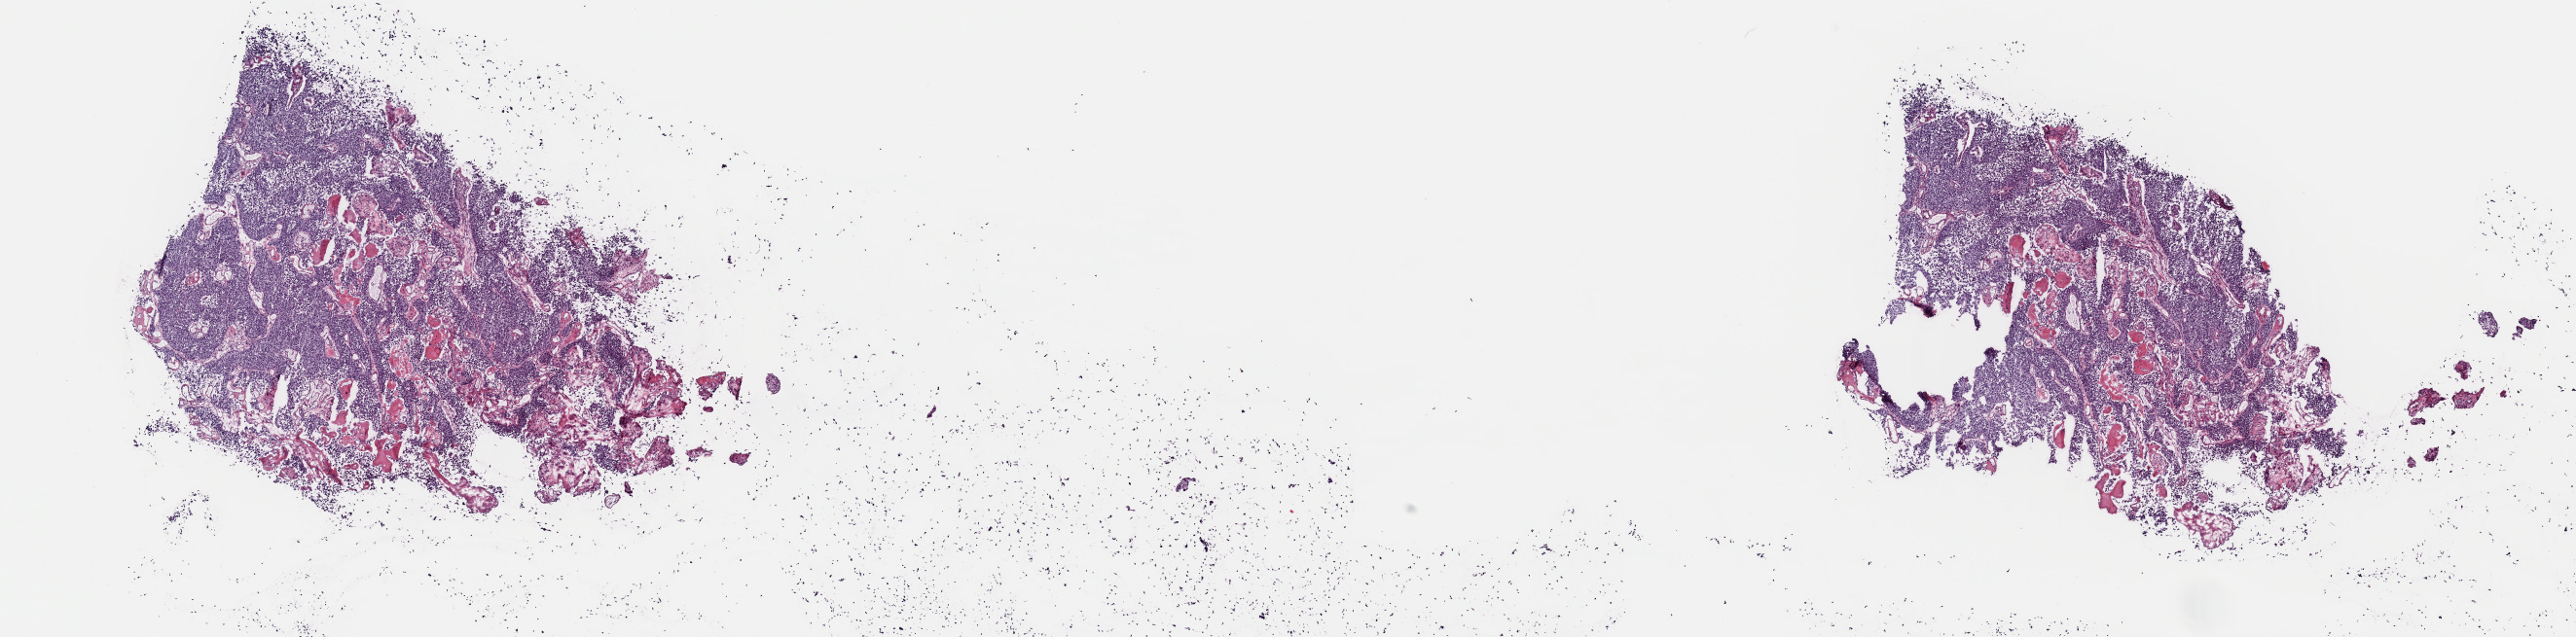
Digitized H&E-stained tissue section (whole slide), whole scanned area (about 20.9 x 5.2 mm, from a 40x scan) shown as a low-resolution overview. Frozen section. Bladder, primary tumour sample. Male, age 77 years at initial diagnosis. Histologic grade: high grade. Slide review estimates, as recorded: tumour cells 95%, tumour nuclei 90%, normal cells 0%, stromal cells 5%, necrosis 0%. Inflammatory infiltration, as recorded: lymphocyte infiltration 1%, monocyte infiltration 0%, neutrophil infiltration 0%.
• TNM: T2a N0 MX
• AJCC pathologic stage: II (7th edition)
• histologic diagnosis: Transitional cell carcinoma
• lymph nodes positive (case pathology): 0 of 19 examined